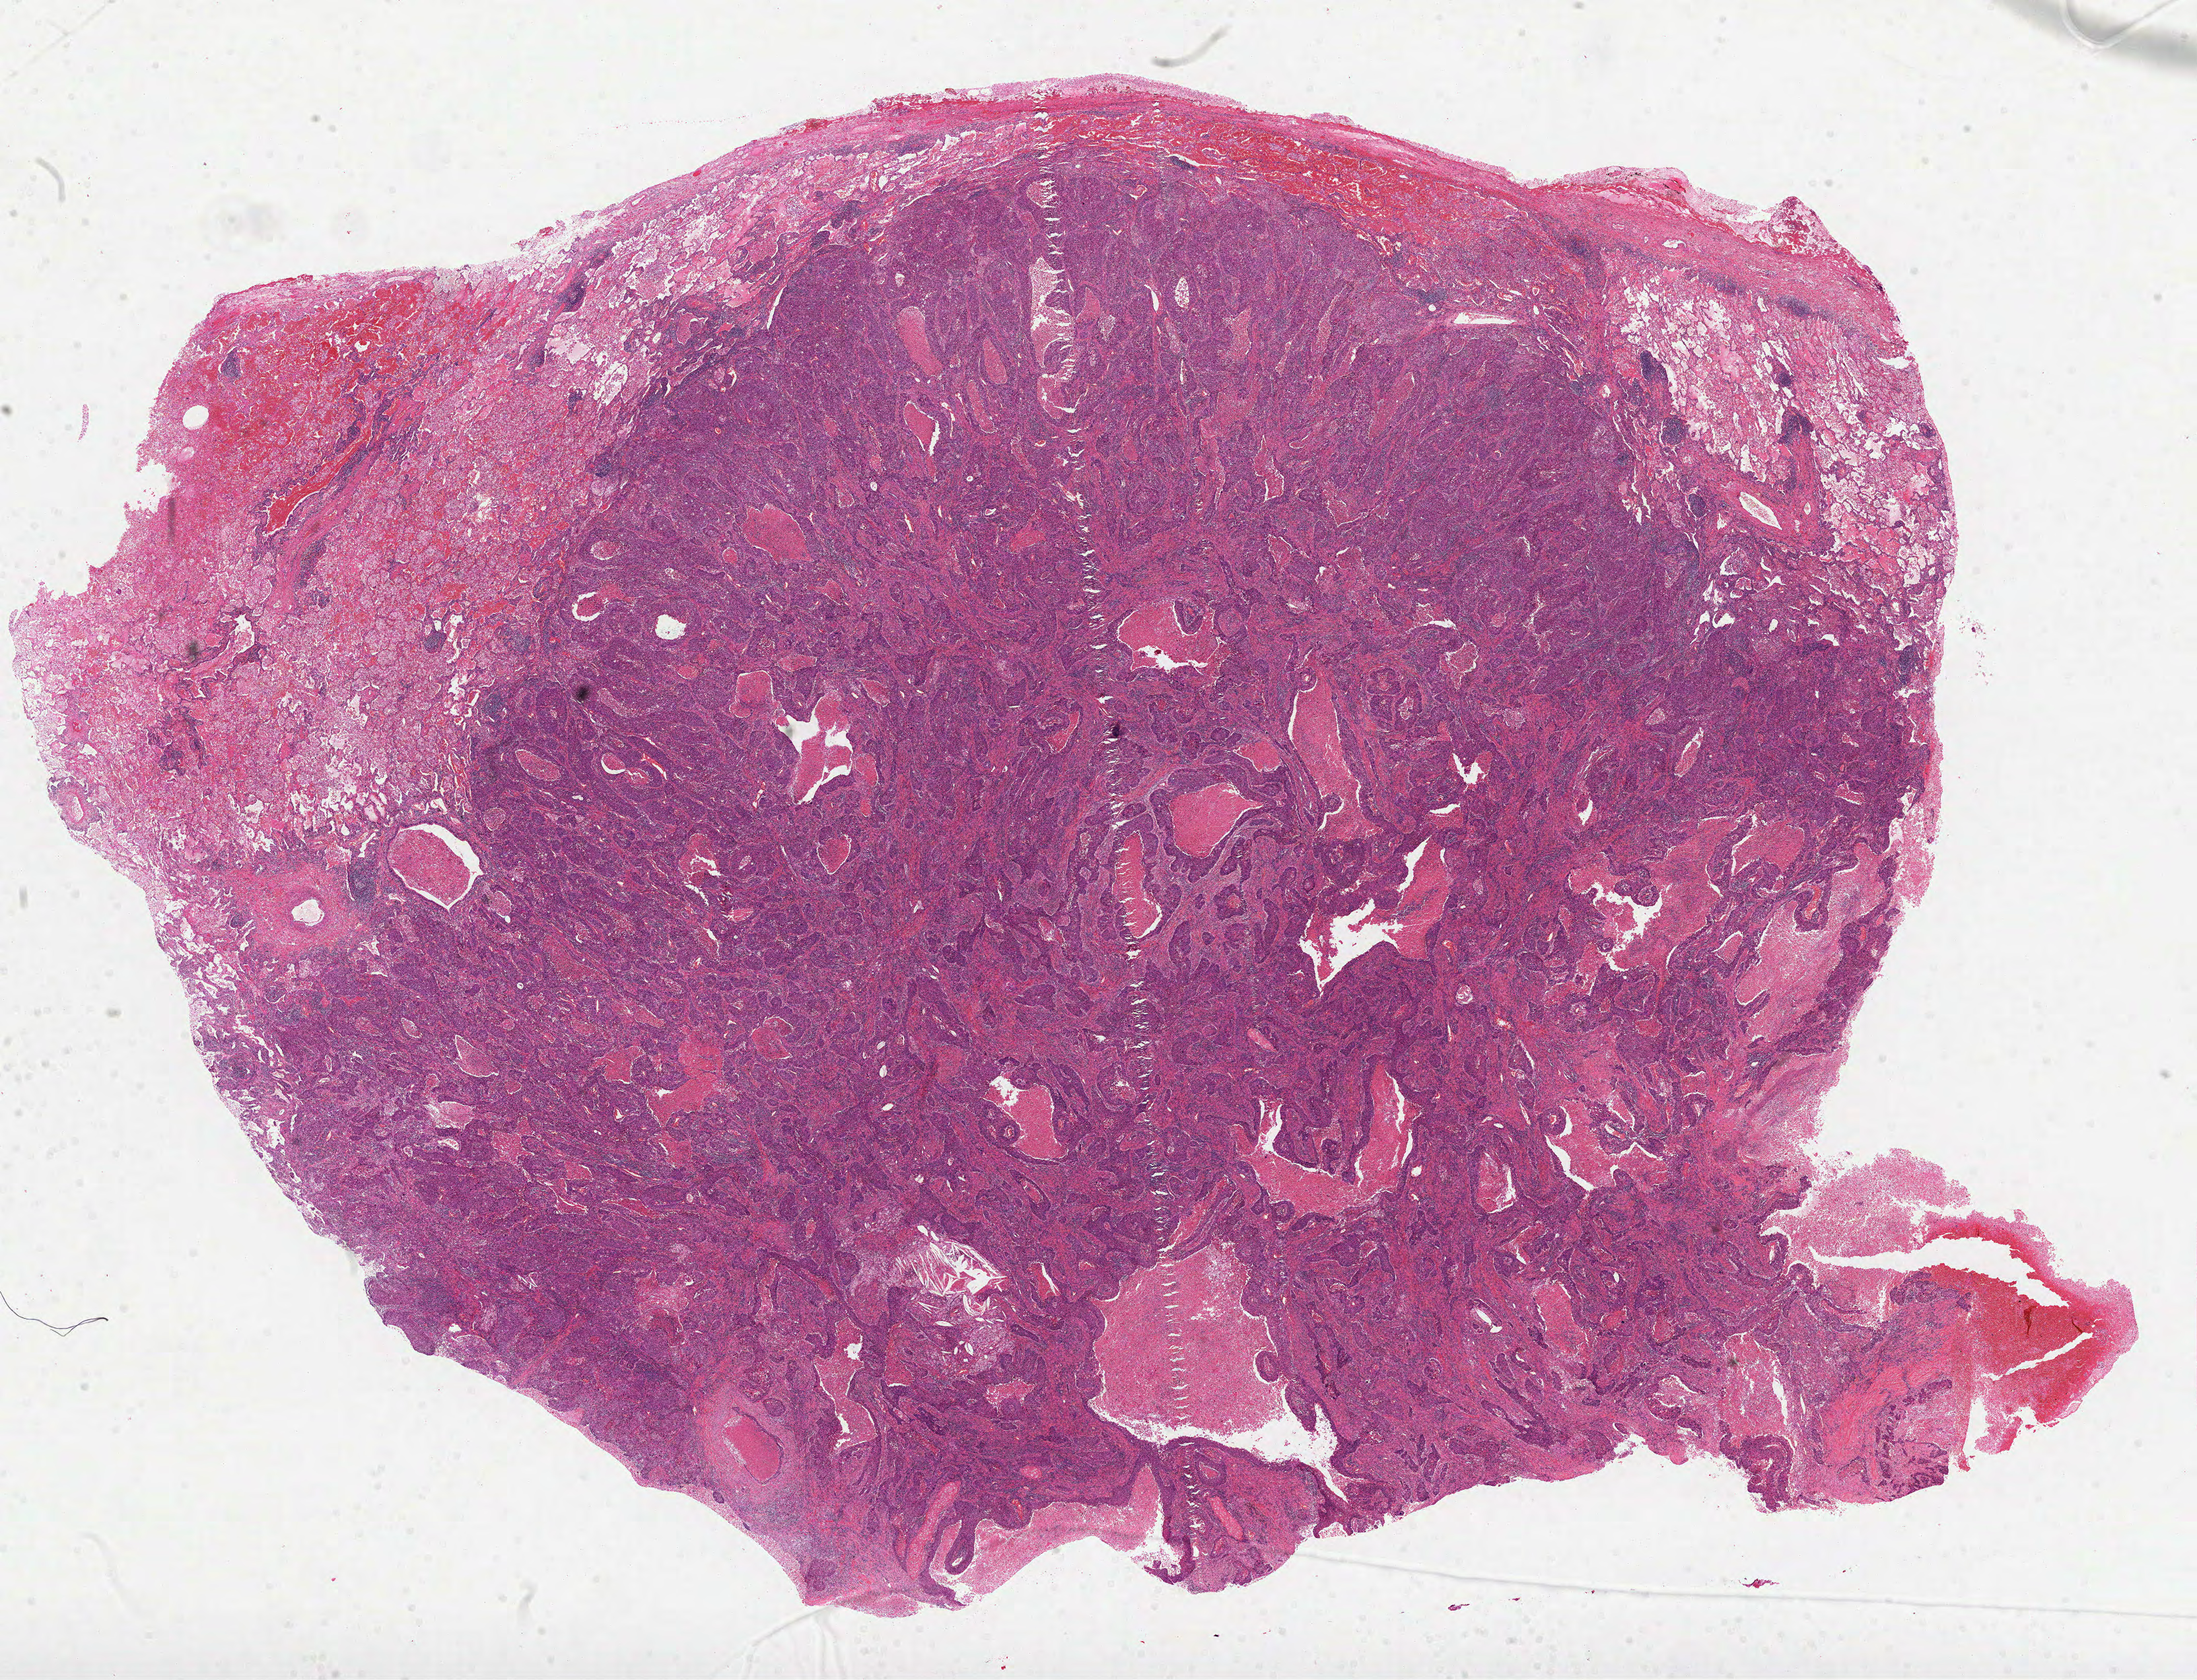
Digitized H&E tissue section (whole slide) — a low-resolution overview of the entire scanned area, about 26.8 x 20.5 mm. Formalin-fixed paraffin-embedded (FFPE) diagnostic section. Sample: primary tumour, lung. Female patient; age at initial diagnosis 69 years.
* histologic diagnosis: Squamous cell carcinoma, NOS
* AJCC pathologic stage: IIB